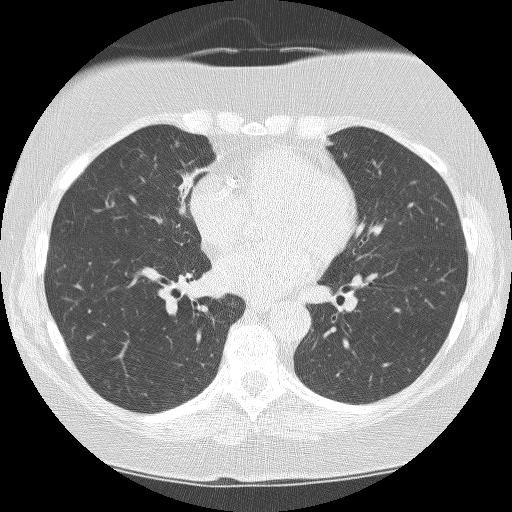
Low-dose screening chest CT, one axial slice. Position 81 of 159 along the scan axis. Reconstruction kernel BONE. 120 kVp. Lung window (W 1500 / L -600 HU). 2.5 mm slice thickness. 512 × 512 image matrix, field of view 299 × 299 mm.
Structures marked on this image (expert manual segmentation):
- lesion 1 (tumor, hilum of right lung): bounding box [x1, y1, x2, y2] px = [176, 168, 210, 214]